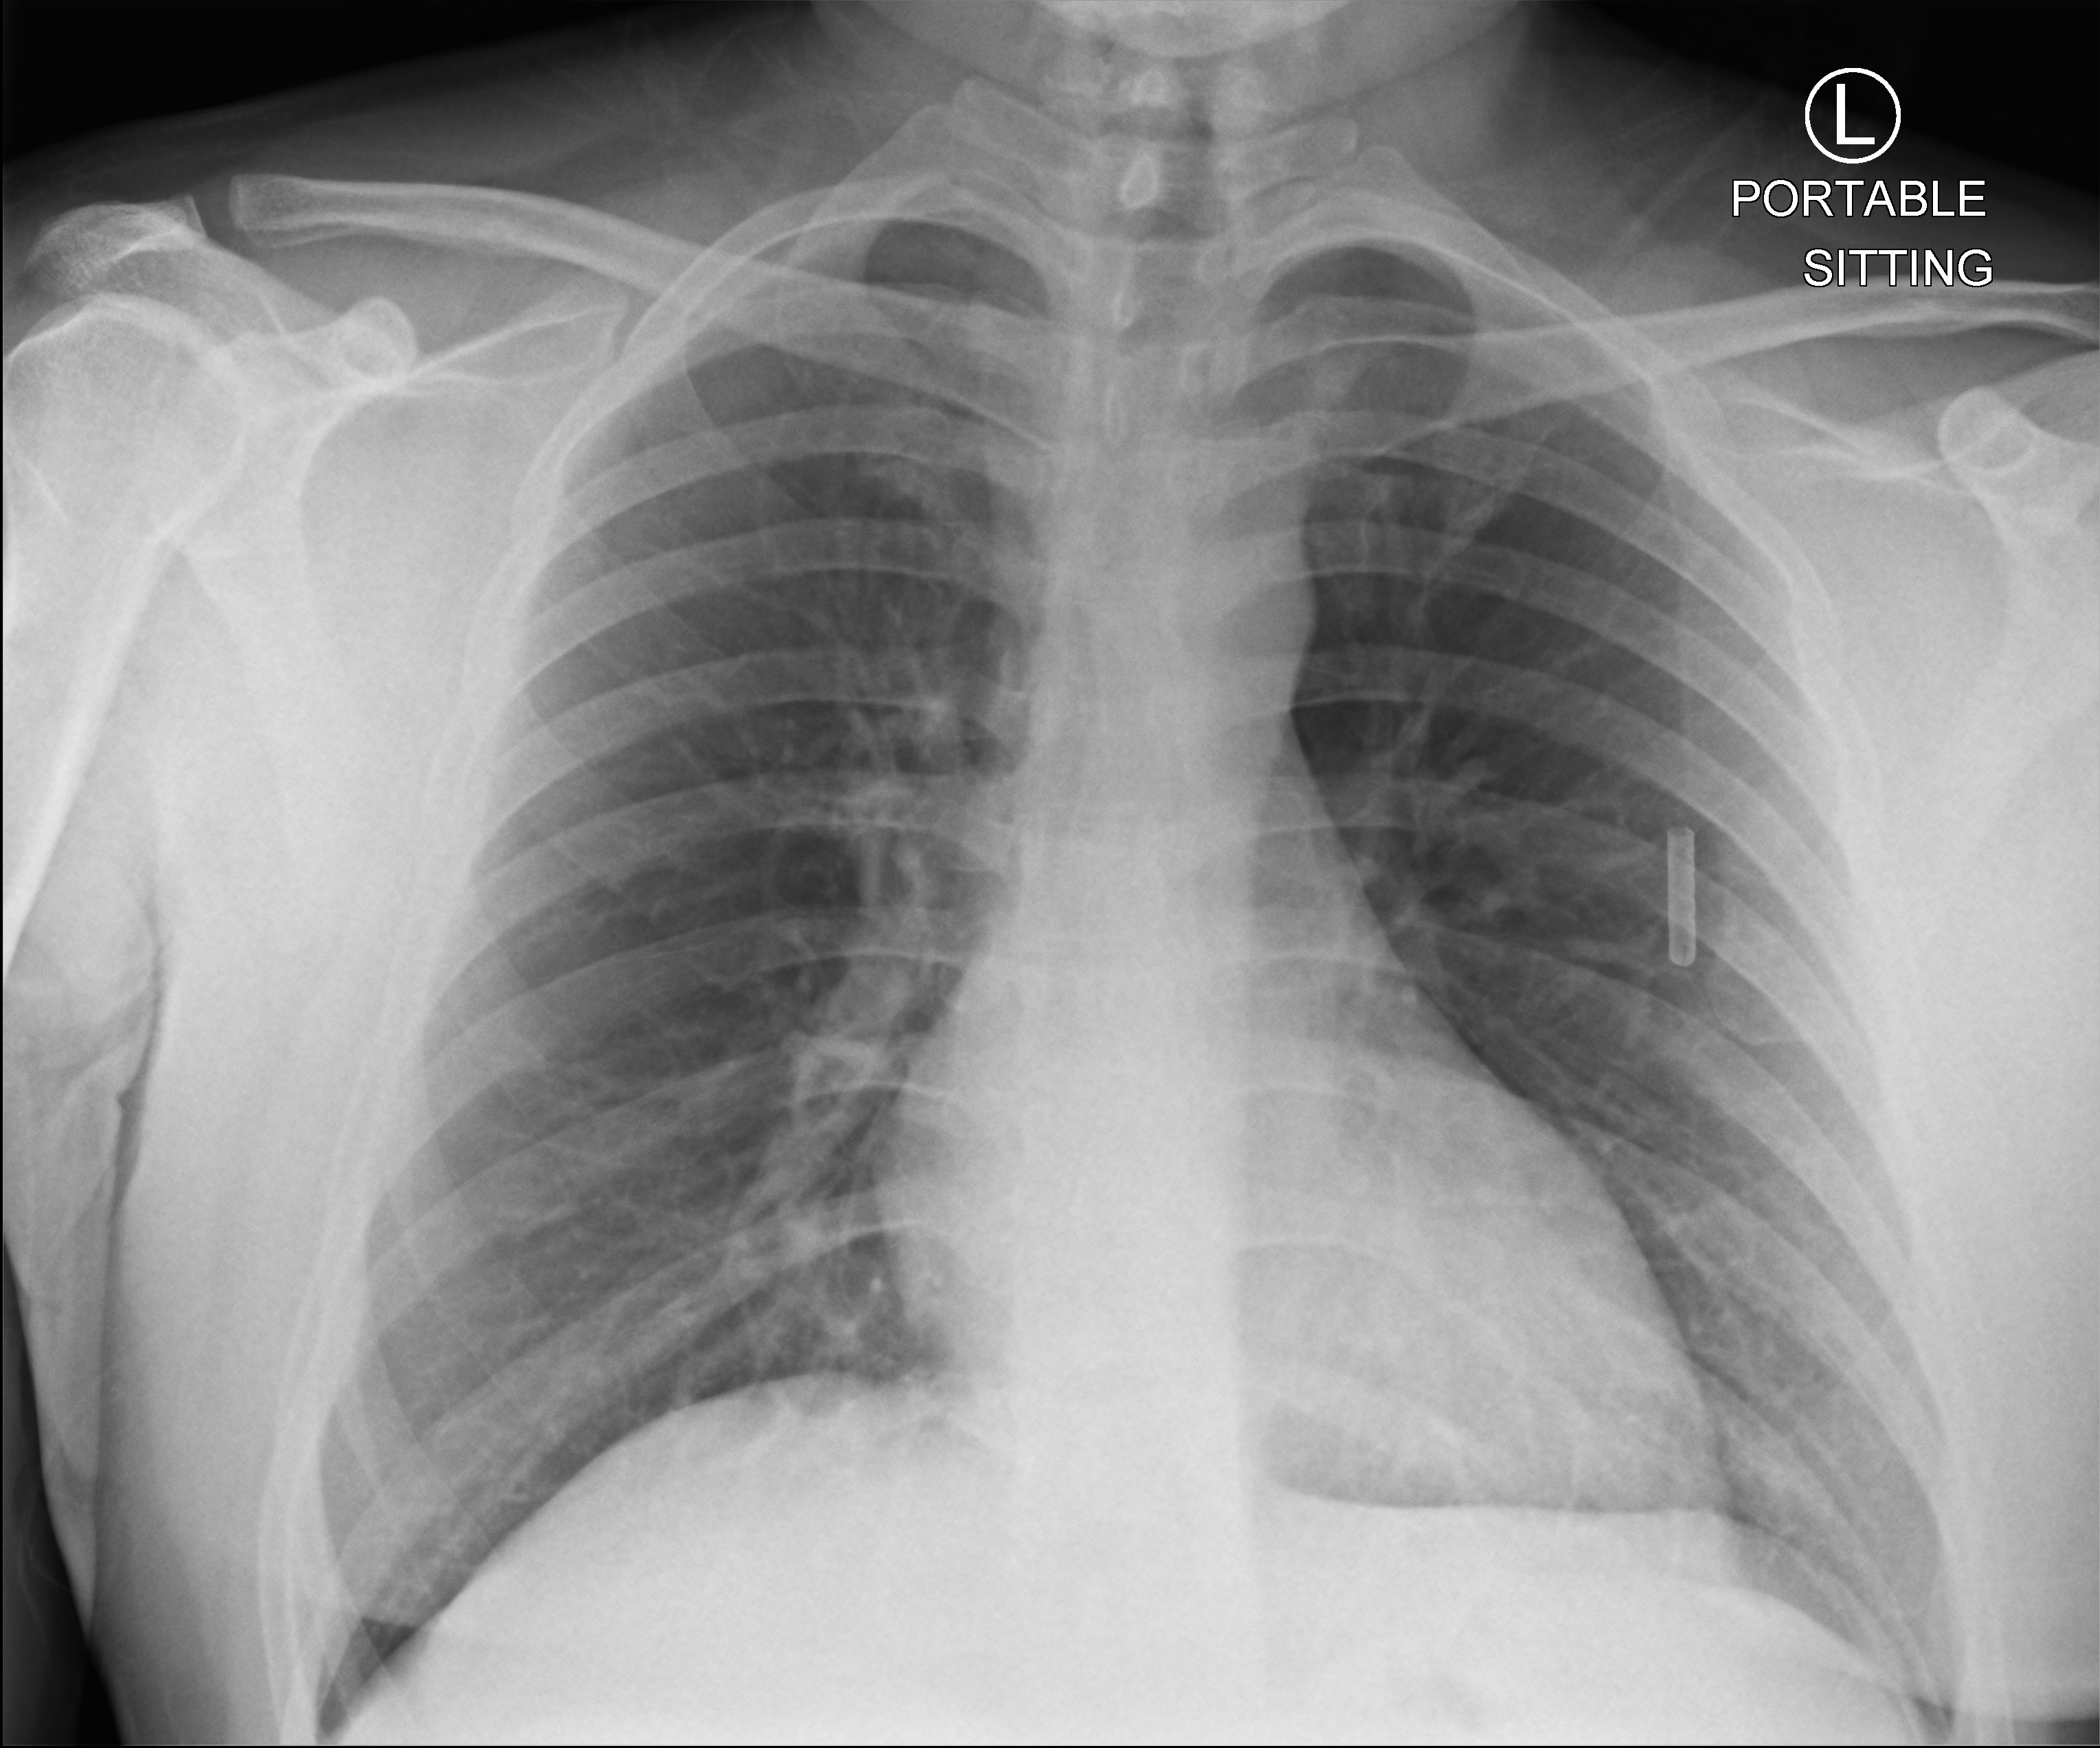
Bedside chest radiograph (computed radiography), anteroposterior (AP) projection. Patient hospitalised with COVID-19; male, aged 18–59 years.
Admission-level facts for this patient (not findings on this image; timing relative to this image not recorded): length of hospital stay: 2 days.